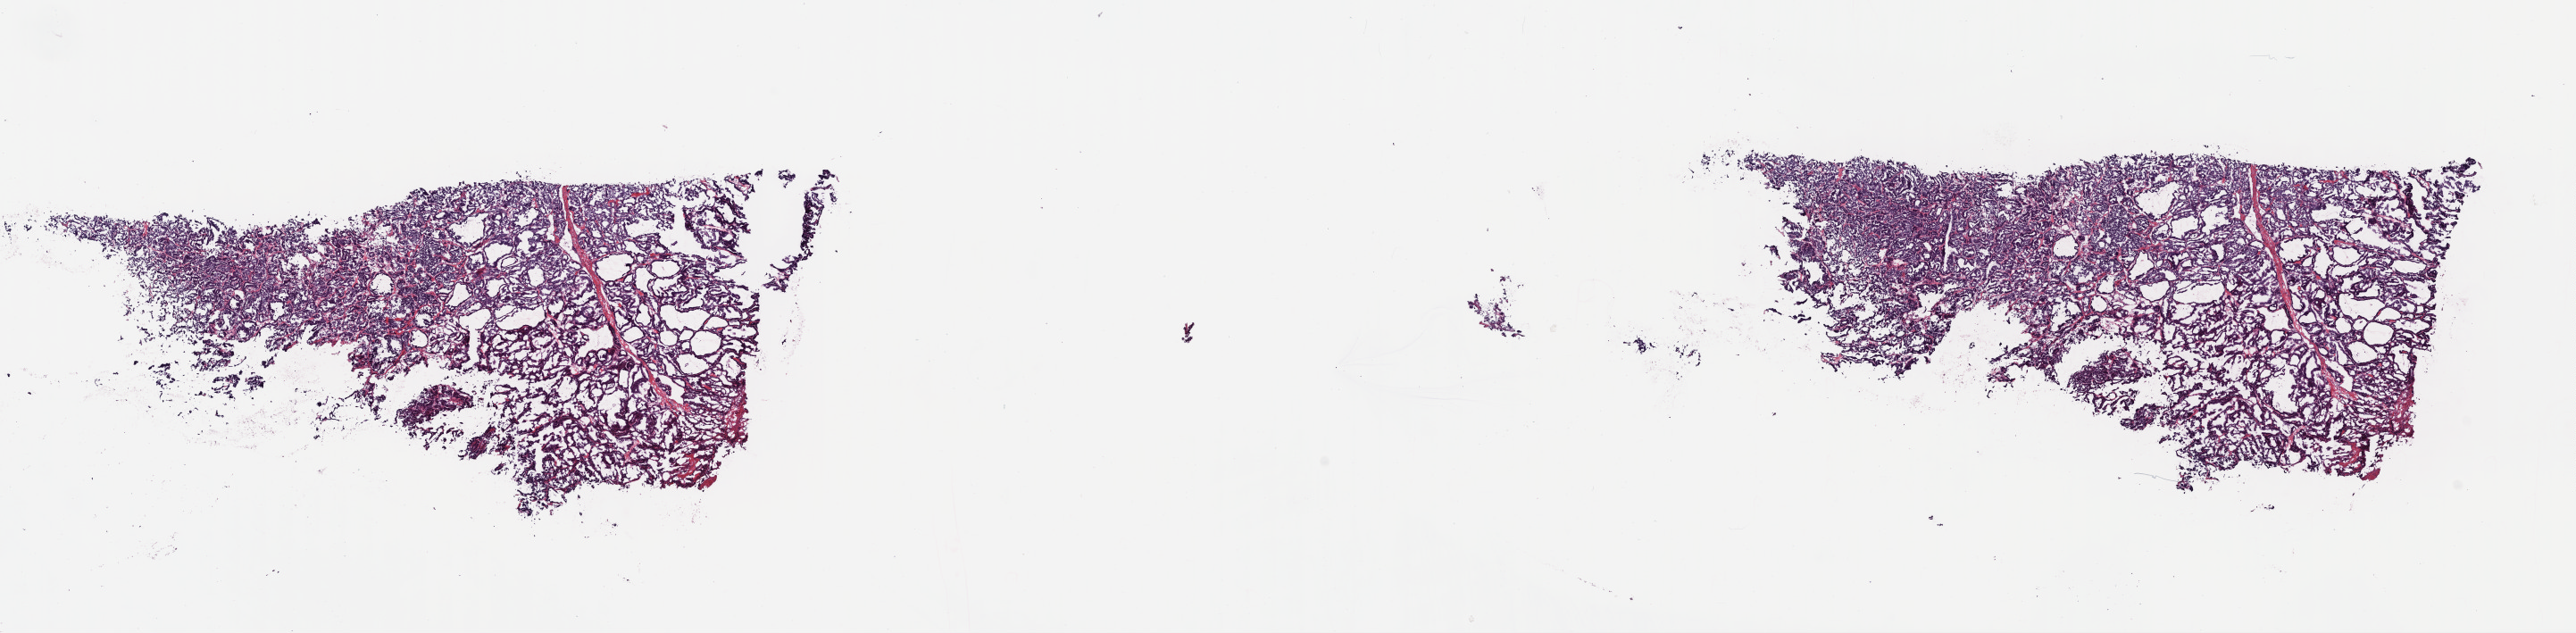
Whole-slide histology image, H&E — a low-resolution overview of the entire scanned area, about 22.7 x 5.6 mm; frozen section from the top of the tissue portion; thyroid, primary tumour sample. Female, age 37 years at initial diagnosis. Pathologist review of this section (percent, as recorded): tumour cells 85%, tumour nuclei 100%, normal cells 0%, stromal cells 15%, necrosis 0%. Infiltration values recorded for this section: lymphocyte infiltration 0%, monocyte infiltration 2%, neutrophil infiltration 0%.
Laterality: right. Pathologic diagnosis: Papillary adenocarcinoma, NOS (thyroid gland). AJCC pathologic stage: I (7th edition). Lymph nodes positive (case pathology): 2 of 4 examined.